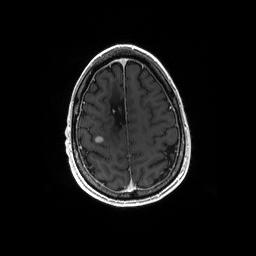
Brain MRI from a brain-tumour surgery series, one axial slice. Slice 47 of 192 in the series (ordered by position). T1-weighted post-contrast. 256 × 256 image matrix, field of view 256 × 256 mm. Case-level facts recorded for this patient, not image findings: histopathology: Astrocytoma; WHO grade: 4; IDH mutation: yes; tumour location: Right Frontal.
Annotated regions visible in this slice (manually delineated by an expert):
- tumour: bounding box [x1, y1, x2, y2] px = [95, 137, 104, 144]